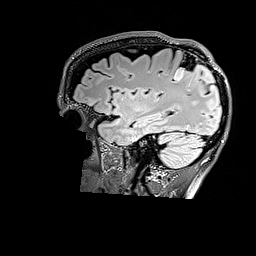
Brain MRI from a brain-tumour surgery series, one sagittal slice; slice 122 of 176 in the series (ordered by position); T2 FLAIR; 1 mm slice thickness; 256 × 256 image matrix. Case-level facts recorded for this patient, not image findings: histopathology: Astrocytoma; WHO grade: 3; IDH mutation: yes.
Structures marked on this image (manually delineated by an expert):
- tumour: bounding box <174,64,211,80> (left, top, right, bottom; pixels)